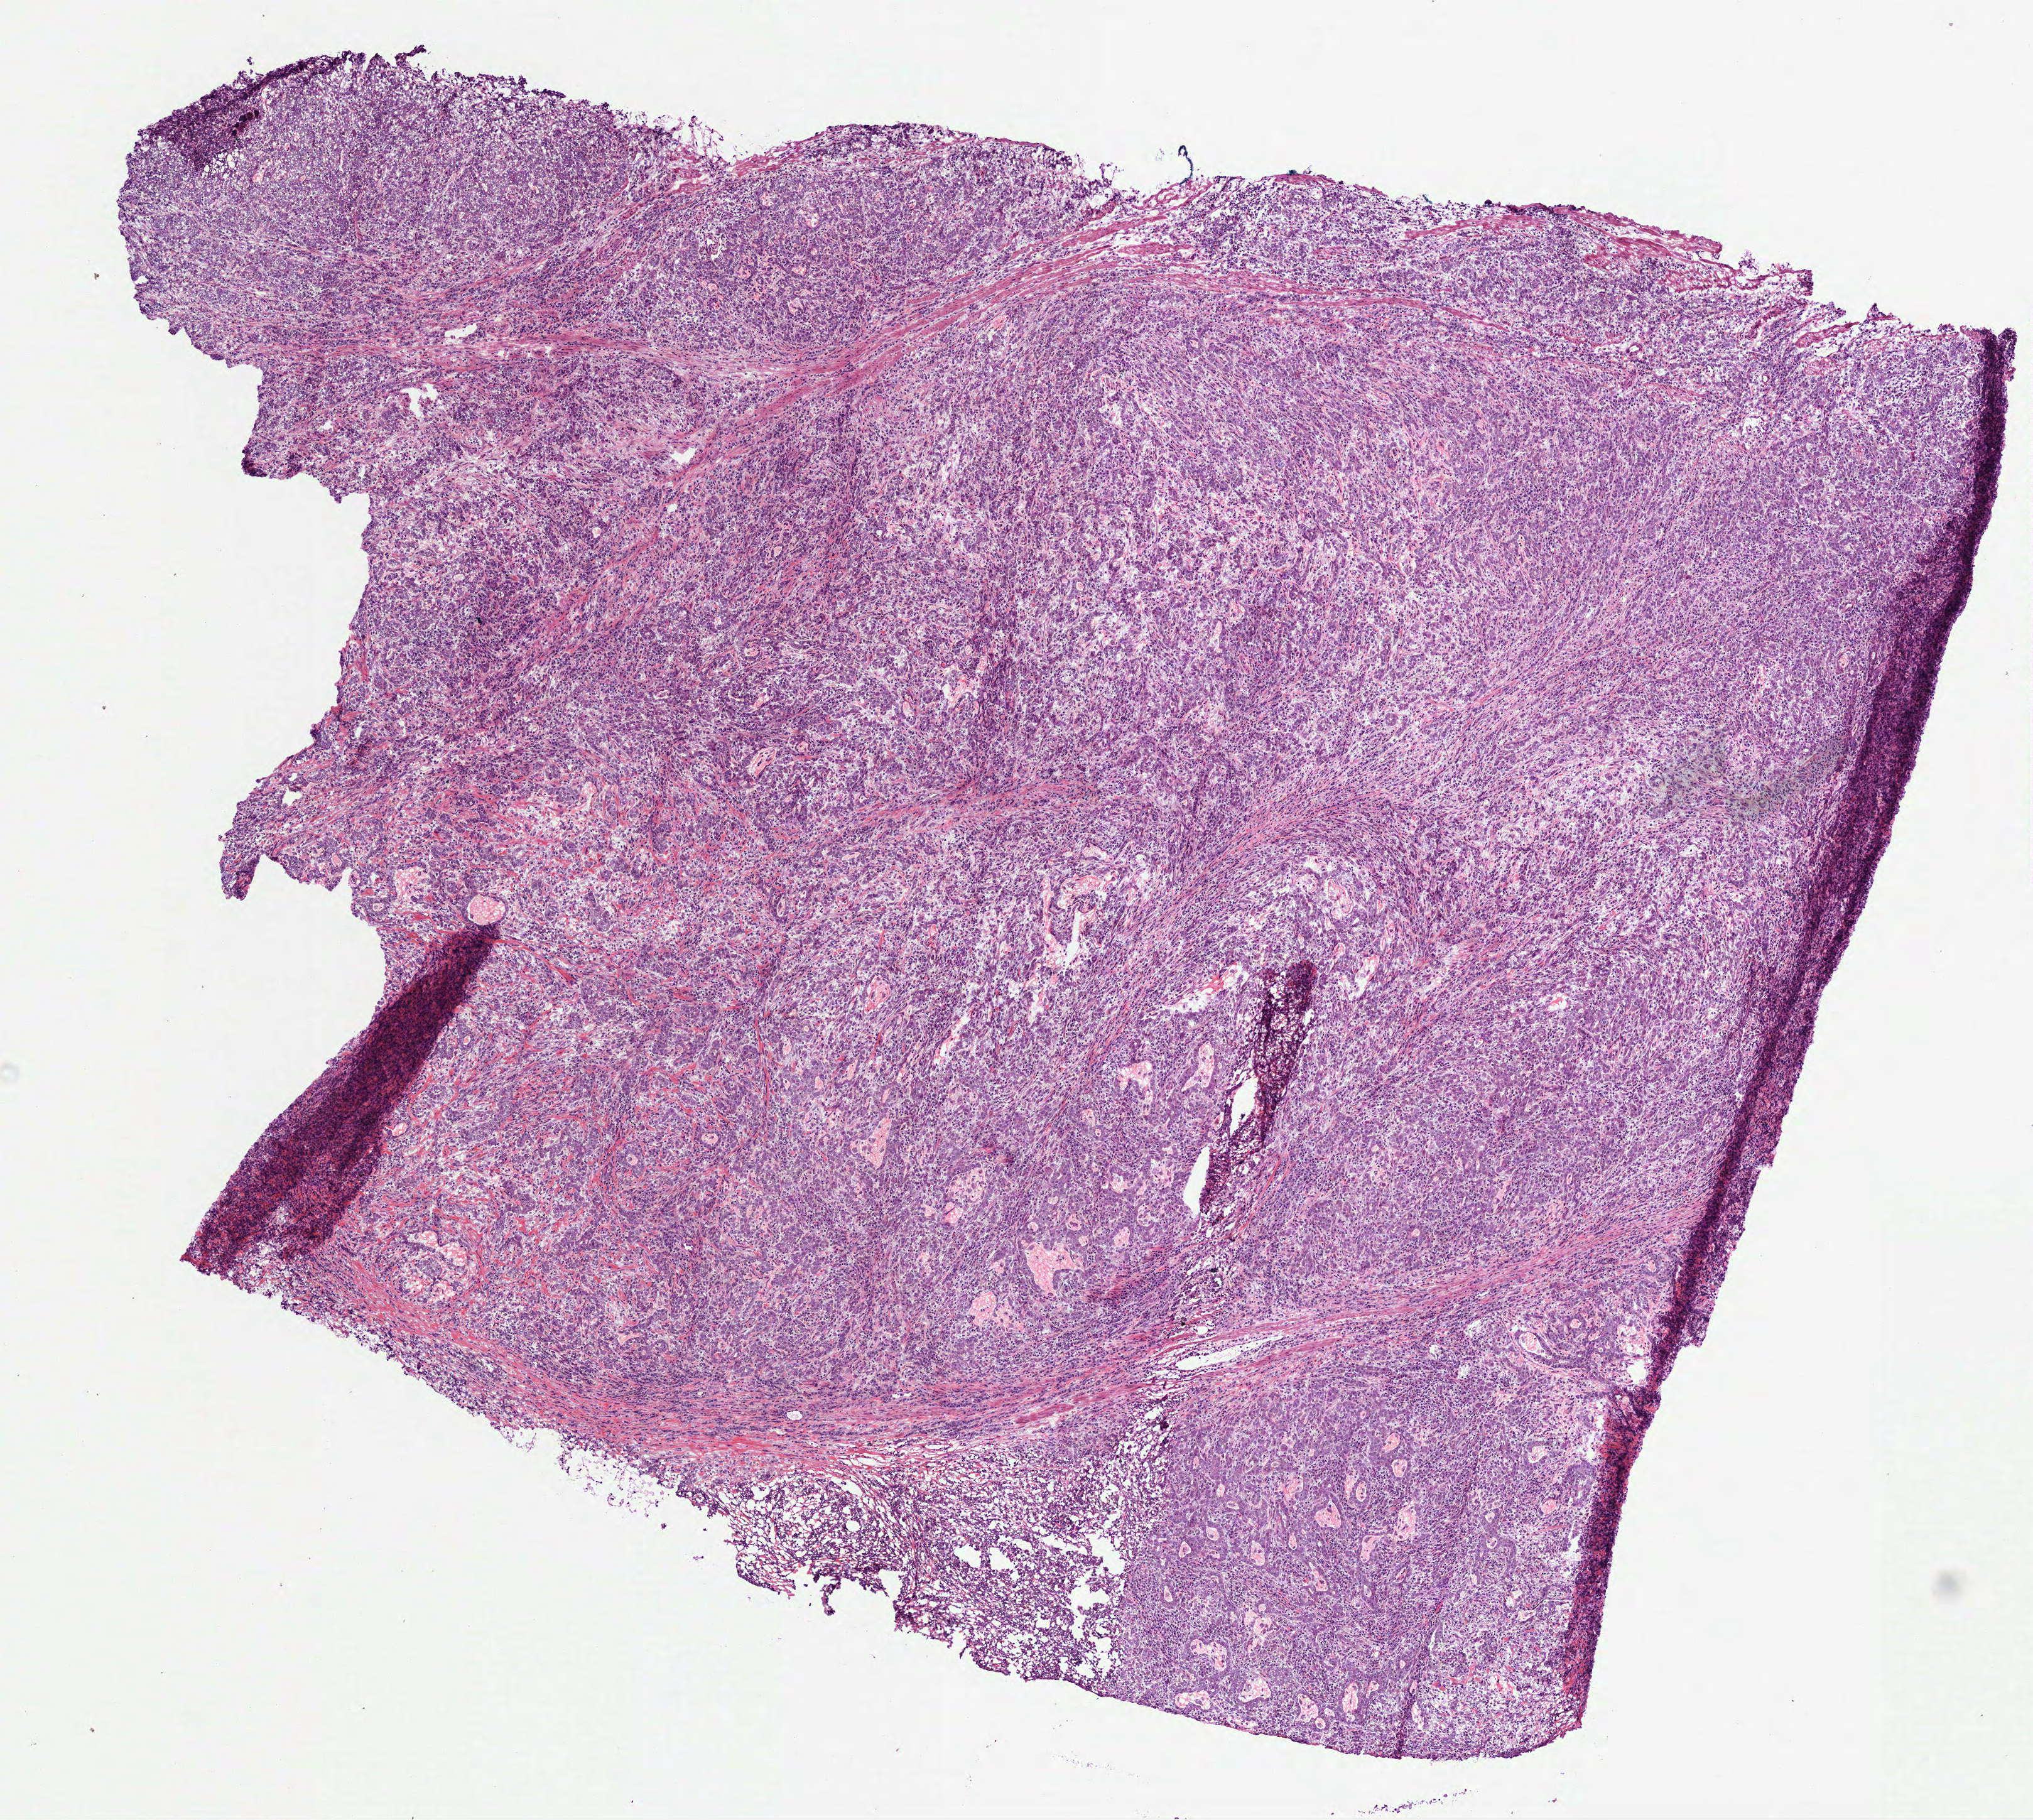
H&E whole-slide image — a low-resolution overview of the entire scanned area, about 6.5 x 5.8 mm (slide scanned at 40x), frozen section from the bottom of the tissue portion, primary tumour sample from the stomach. Male patient; age at initial diagnosis 44 years.
Histologic diagnosis: Tubular adenocarcinoma (cardia, NOS).